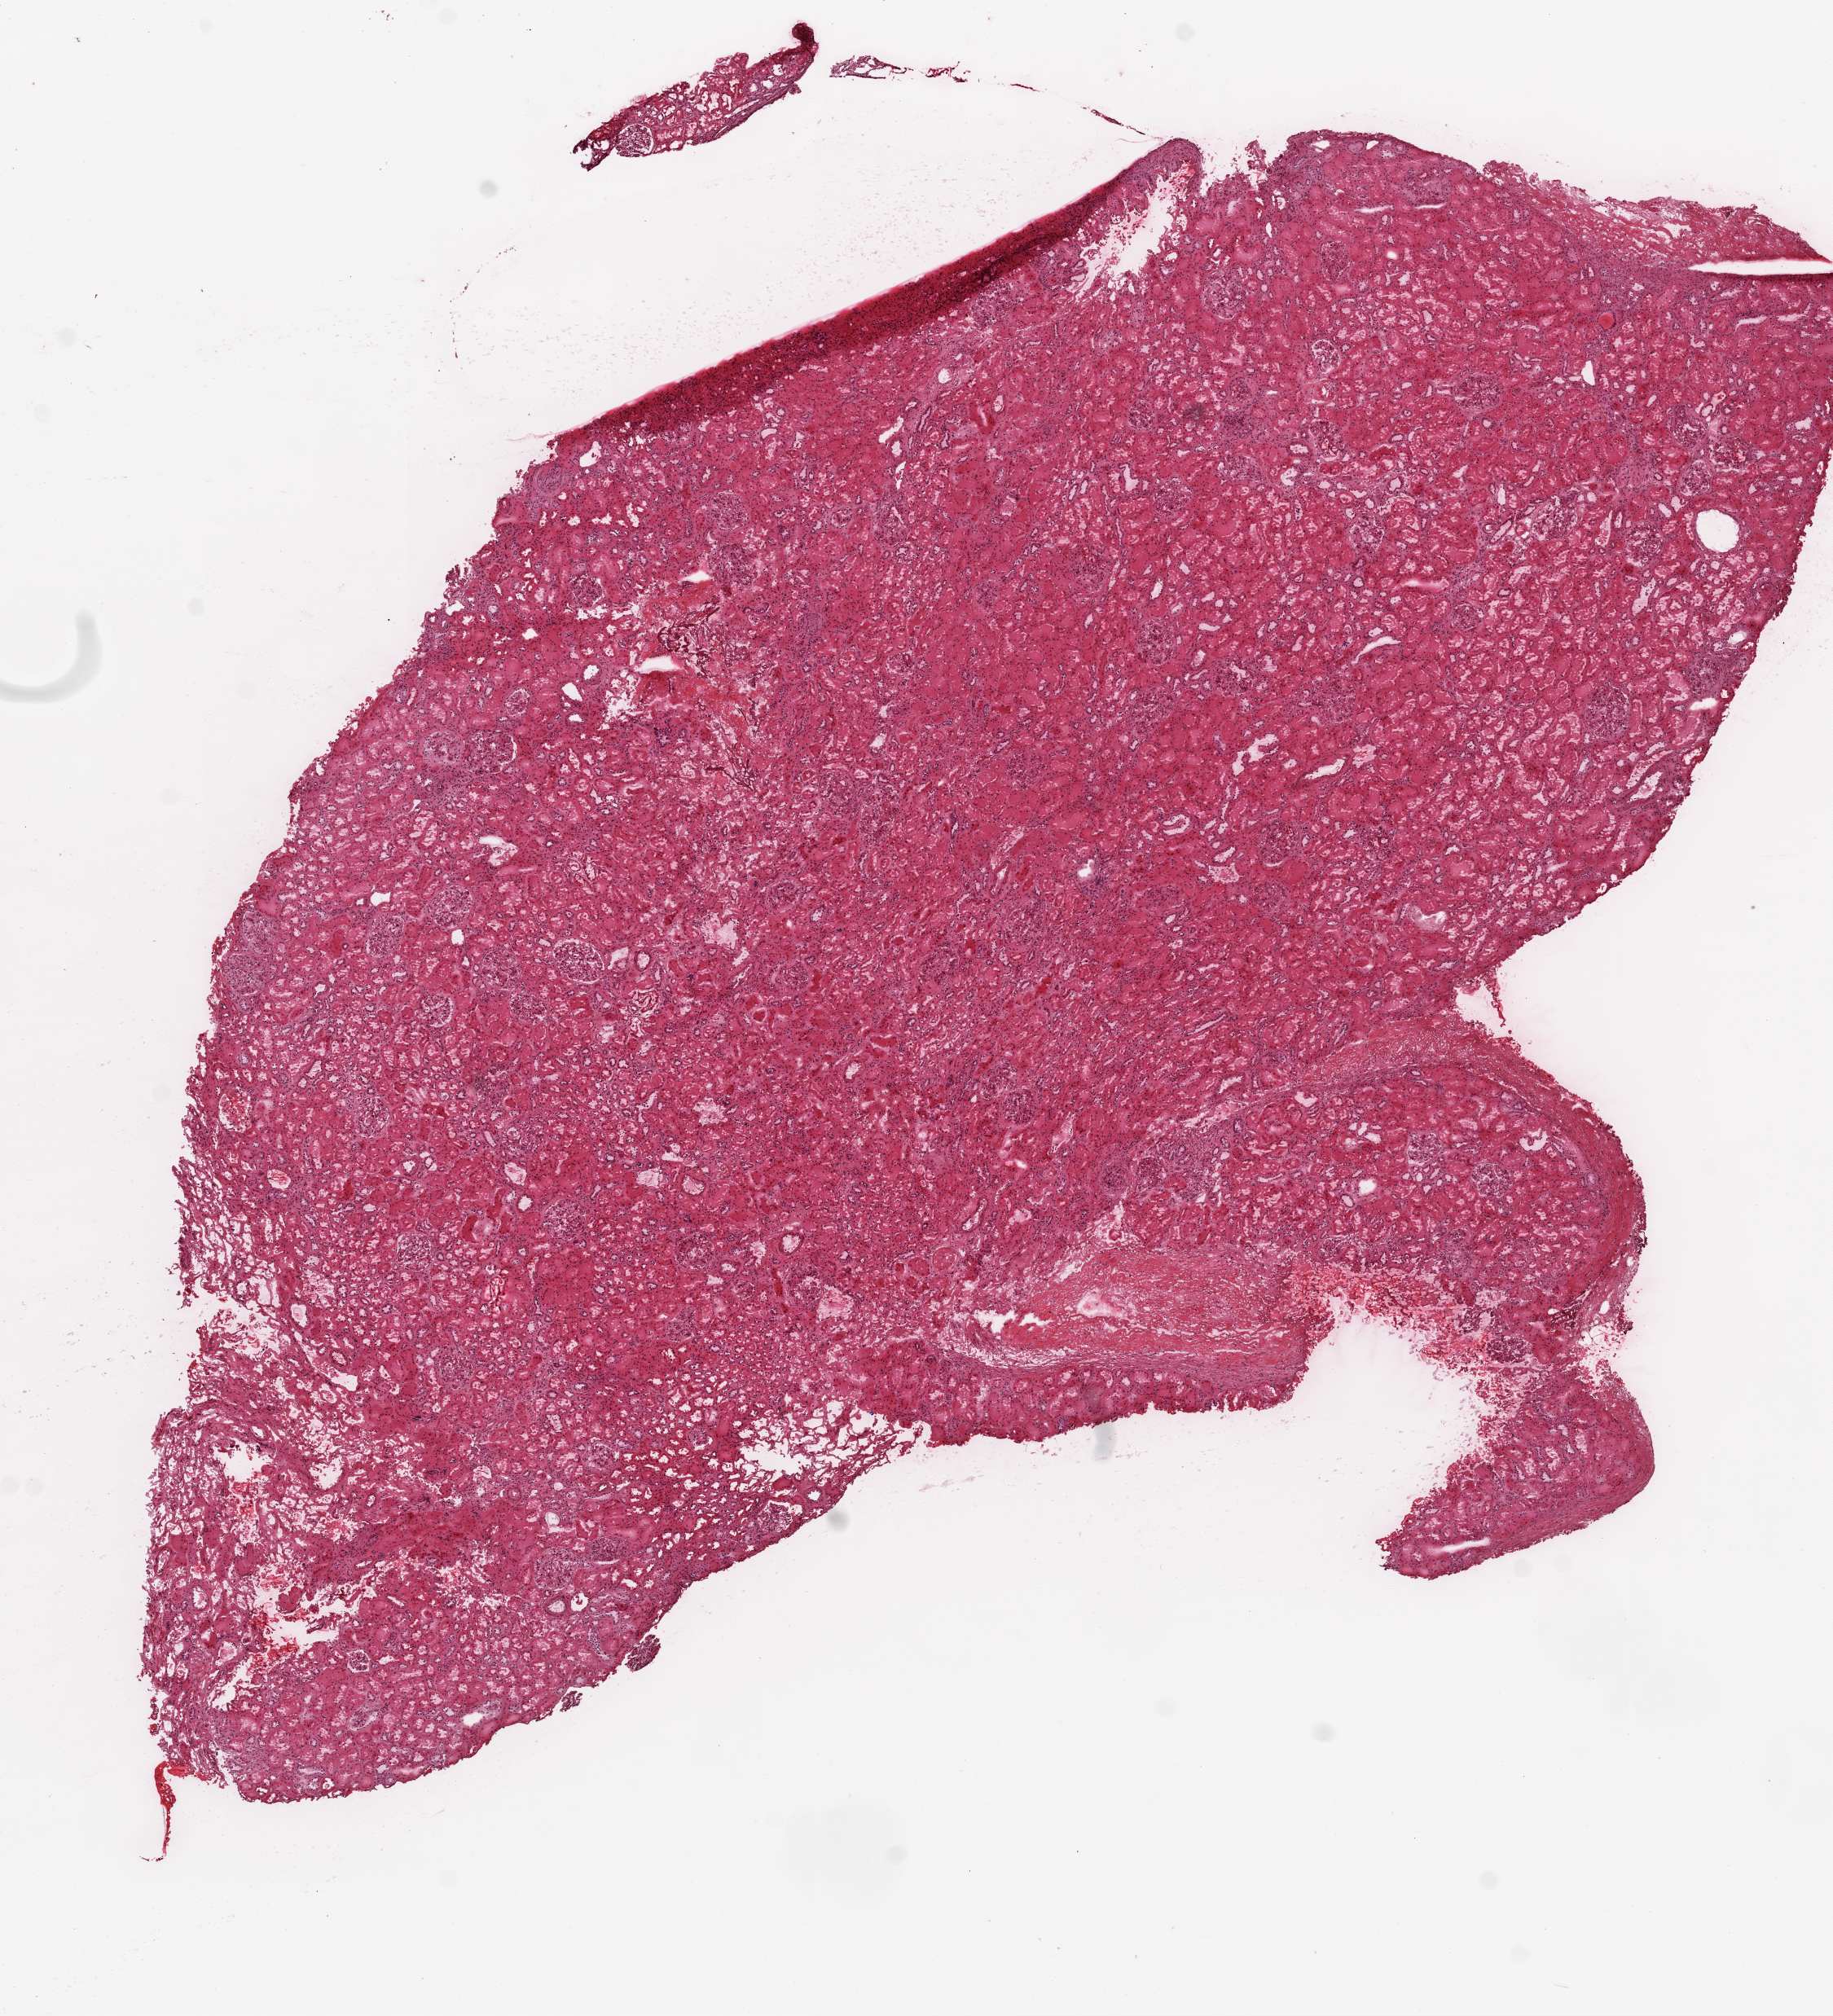
Hematoxylin and eosin (H&E) stained whole-slide image — whole scanned area (about 9.0 x 9.9 mm) shown as a low-resolution overview. Frozen section. Solid tissue normal (non-tumour tissue) sample from the kidney. Male patient; age at initial diagnosis 56 years.
This section: solid tissue normal sample (biorepository sample class). Patient diagnosis: Clear cell adenocarcinoma, NOS.